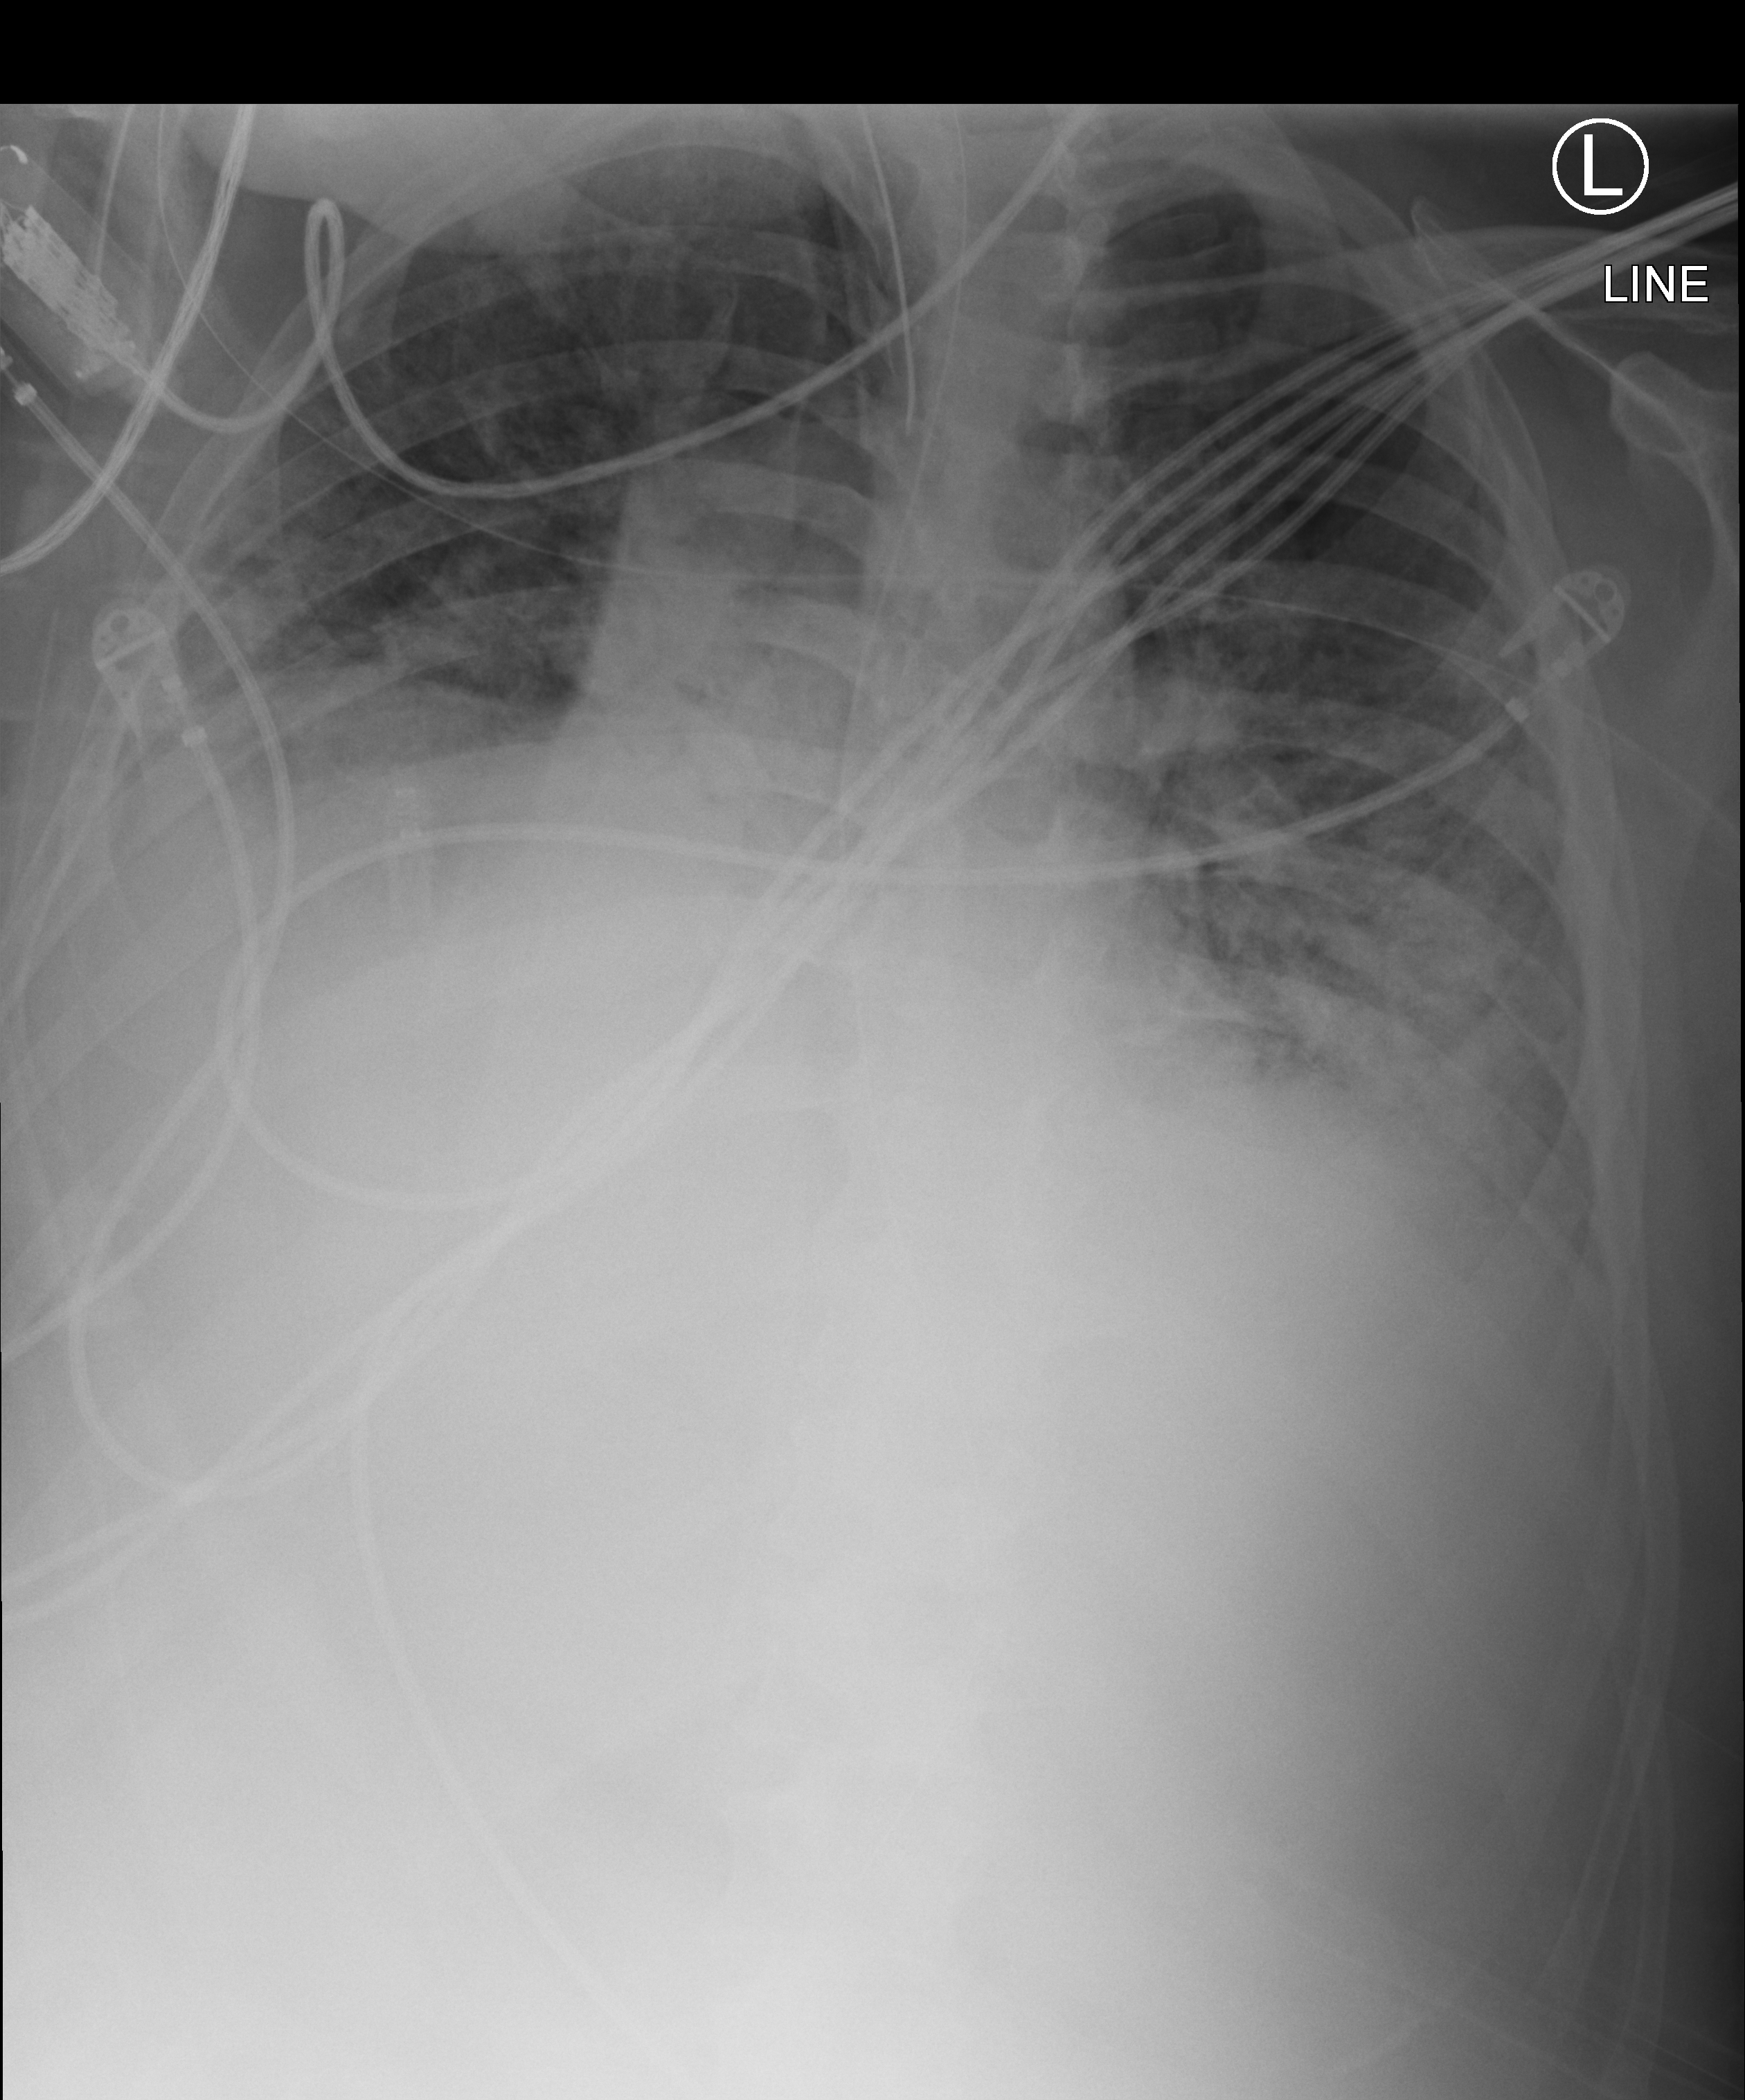
Bedside chest radiograph (computed radiography), anteroposterior (AP) projection. Patient hospitalised with COVID-19; male, aged 18–59 years.
Admission-level facts for this patient (not findings on this image; timing relative to this image not recorded): hypertension (admission record): yes.